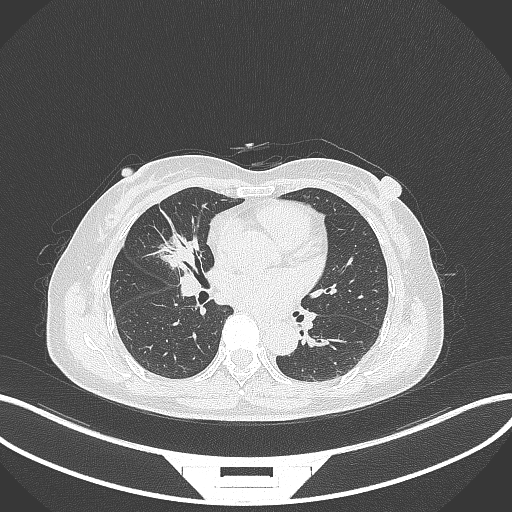
Chest CT, one axial slice. Slice 149 of 284 in the series (ordered by position). Lung window (W 1500 / L -600 HU). 1 mm slice thickness. 512 × 512 image matrix, field of view 400 × 400 mm. Female patient, age 51 years. From the clinical record (not read from this slice): clinical TNM (as recorded): T1c N0 M0.
Annotated regions visible in this slice (rectangle marked by the reading radiologist):
- lung tumour (recorded histology: adenocarcinoma): bounding box [x1, y1, x2, y2] px = [156, 225, 203, 272]